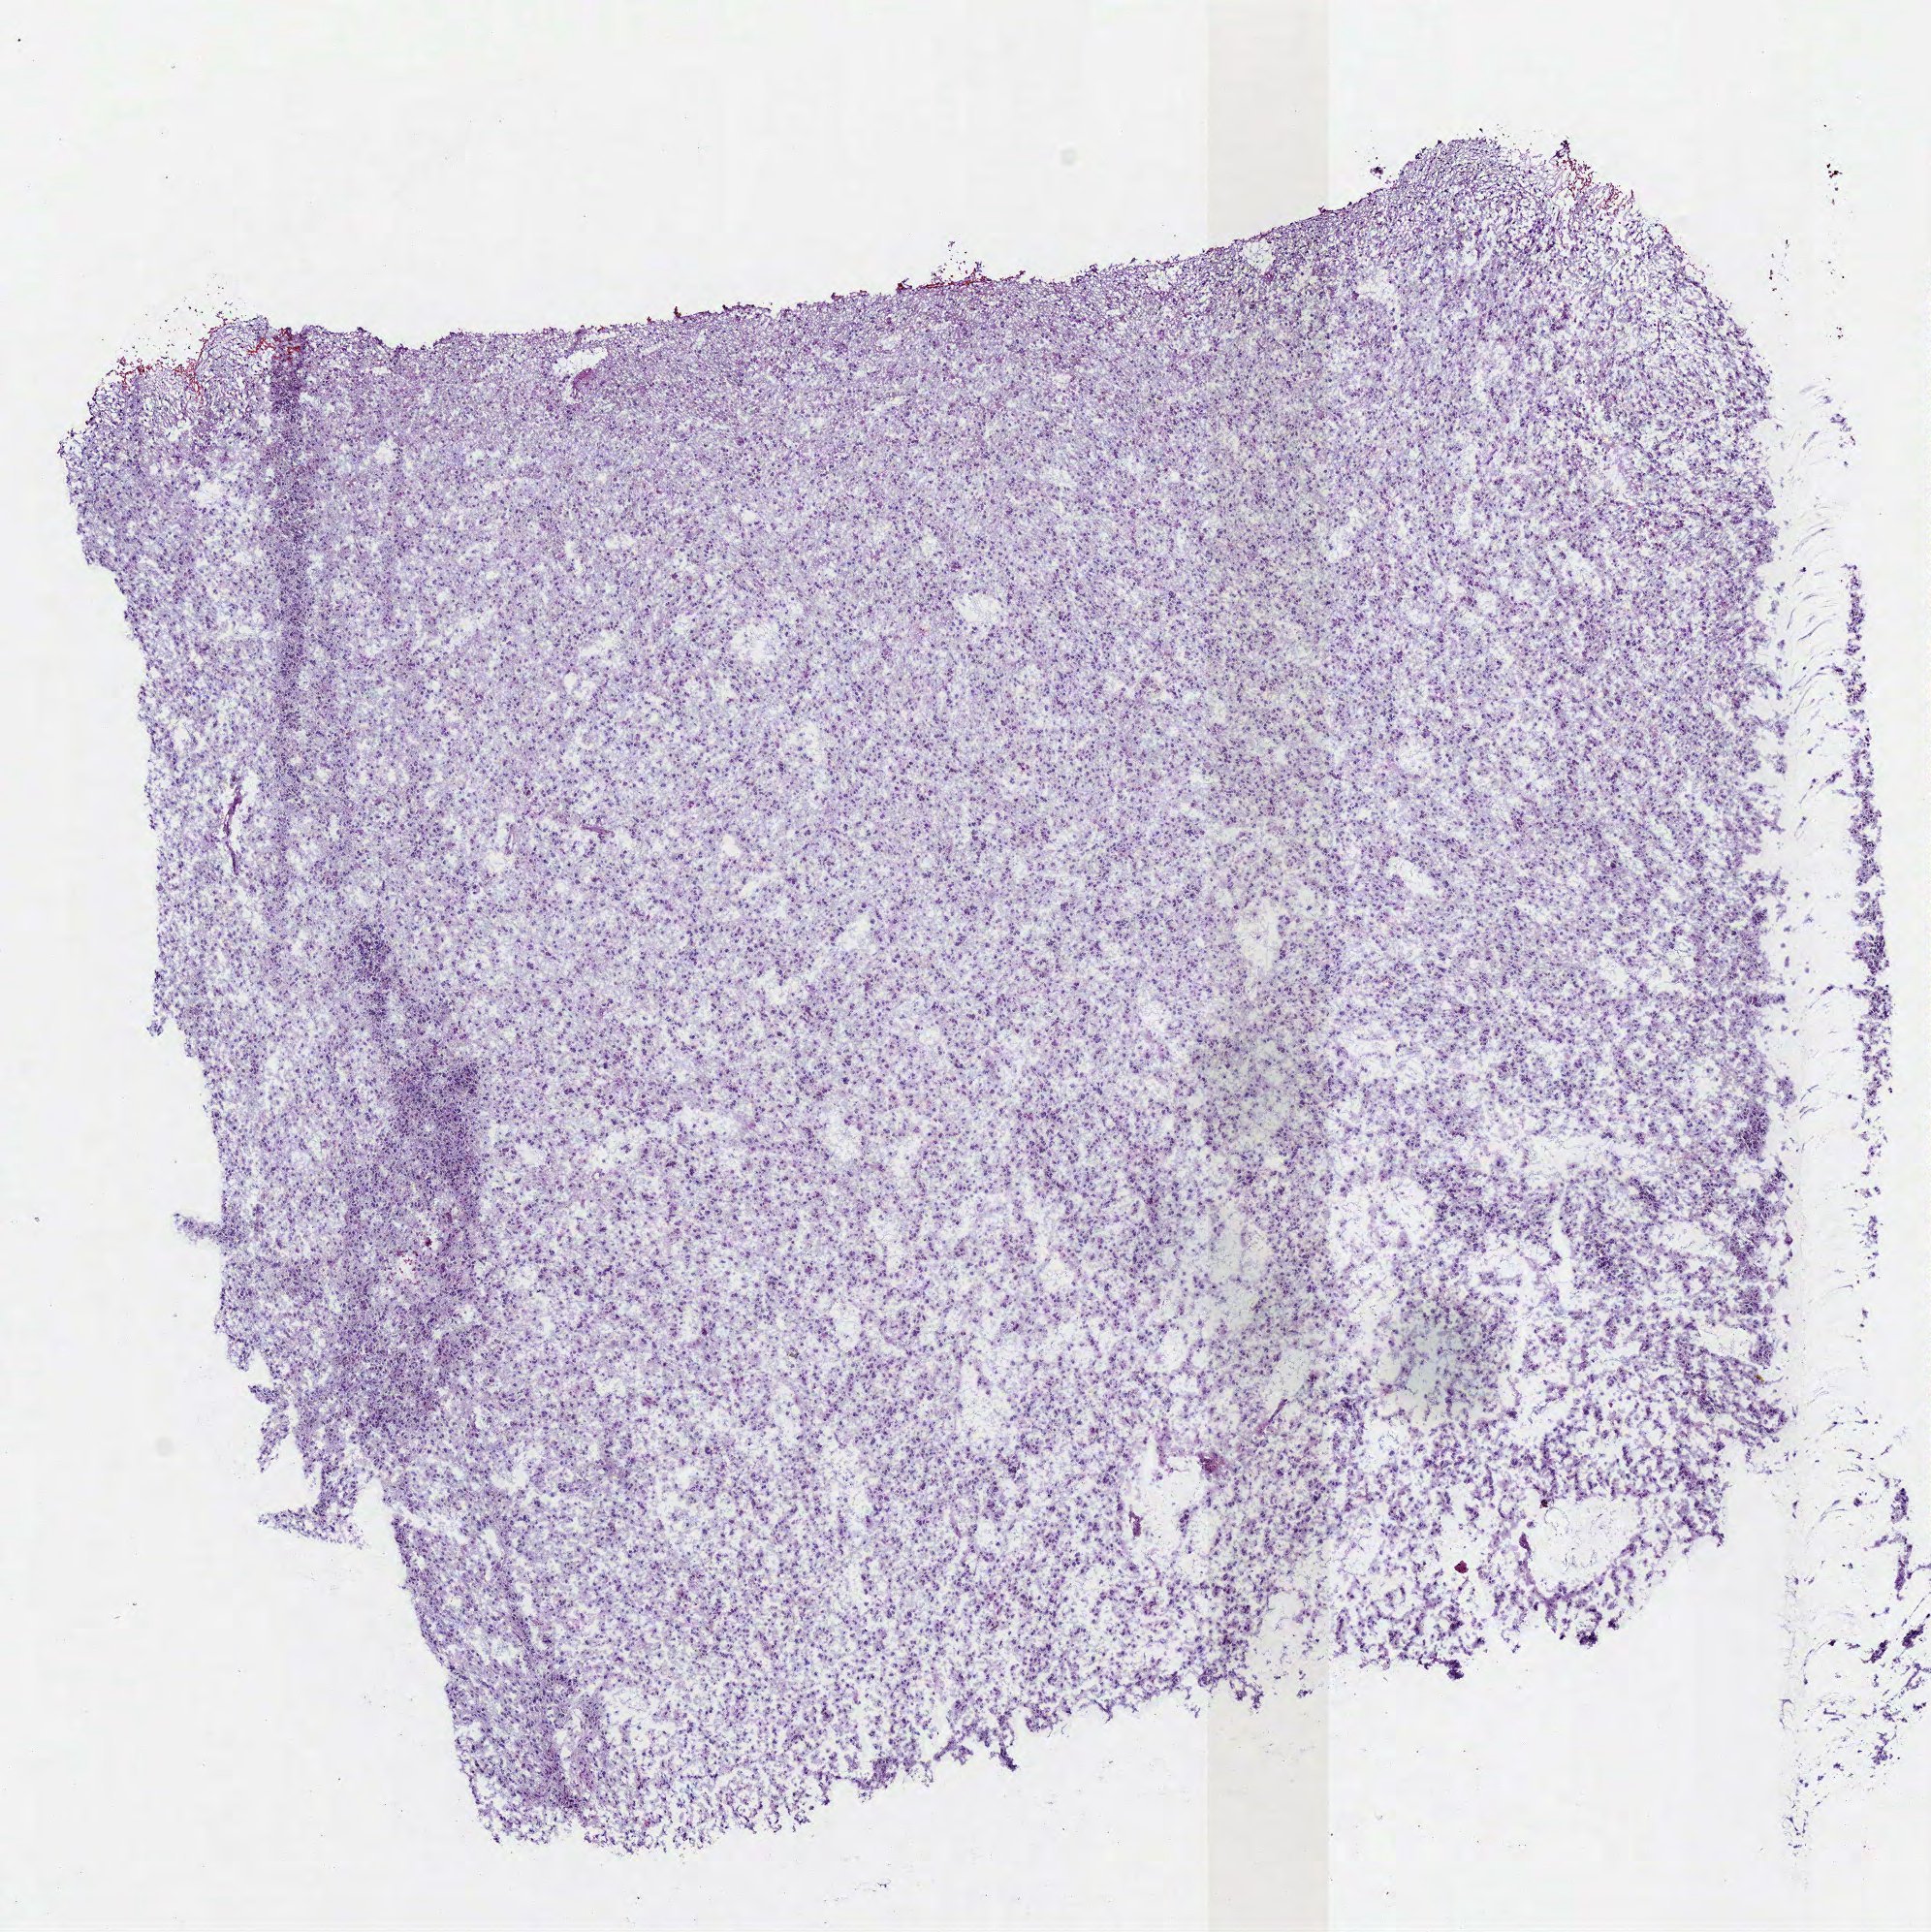
Digitized Hematoxylin and eosin (H&E) stained tissue section (whole slide), low-resolution overview of the scanned area, about 7.8 x 7.8 mm, frozen section from the top of the tissue portion, sample: primary tumour, brain. Female patient; age at initial diagnosis 41 years. Histologic grade: G2 (moderately differentiated). Pathologist review of this section (percent, as recorded): tumour cells 100%, tumour nuclei 80%, normal cells 0%, stromal cells 0%, necrosis 0%.
• histologic diagnosis: Oligodendroglioma, NOS (cerebrum)